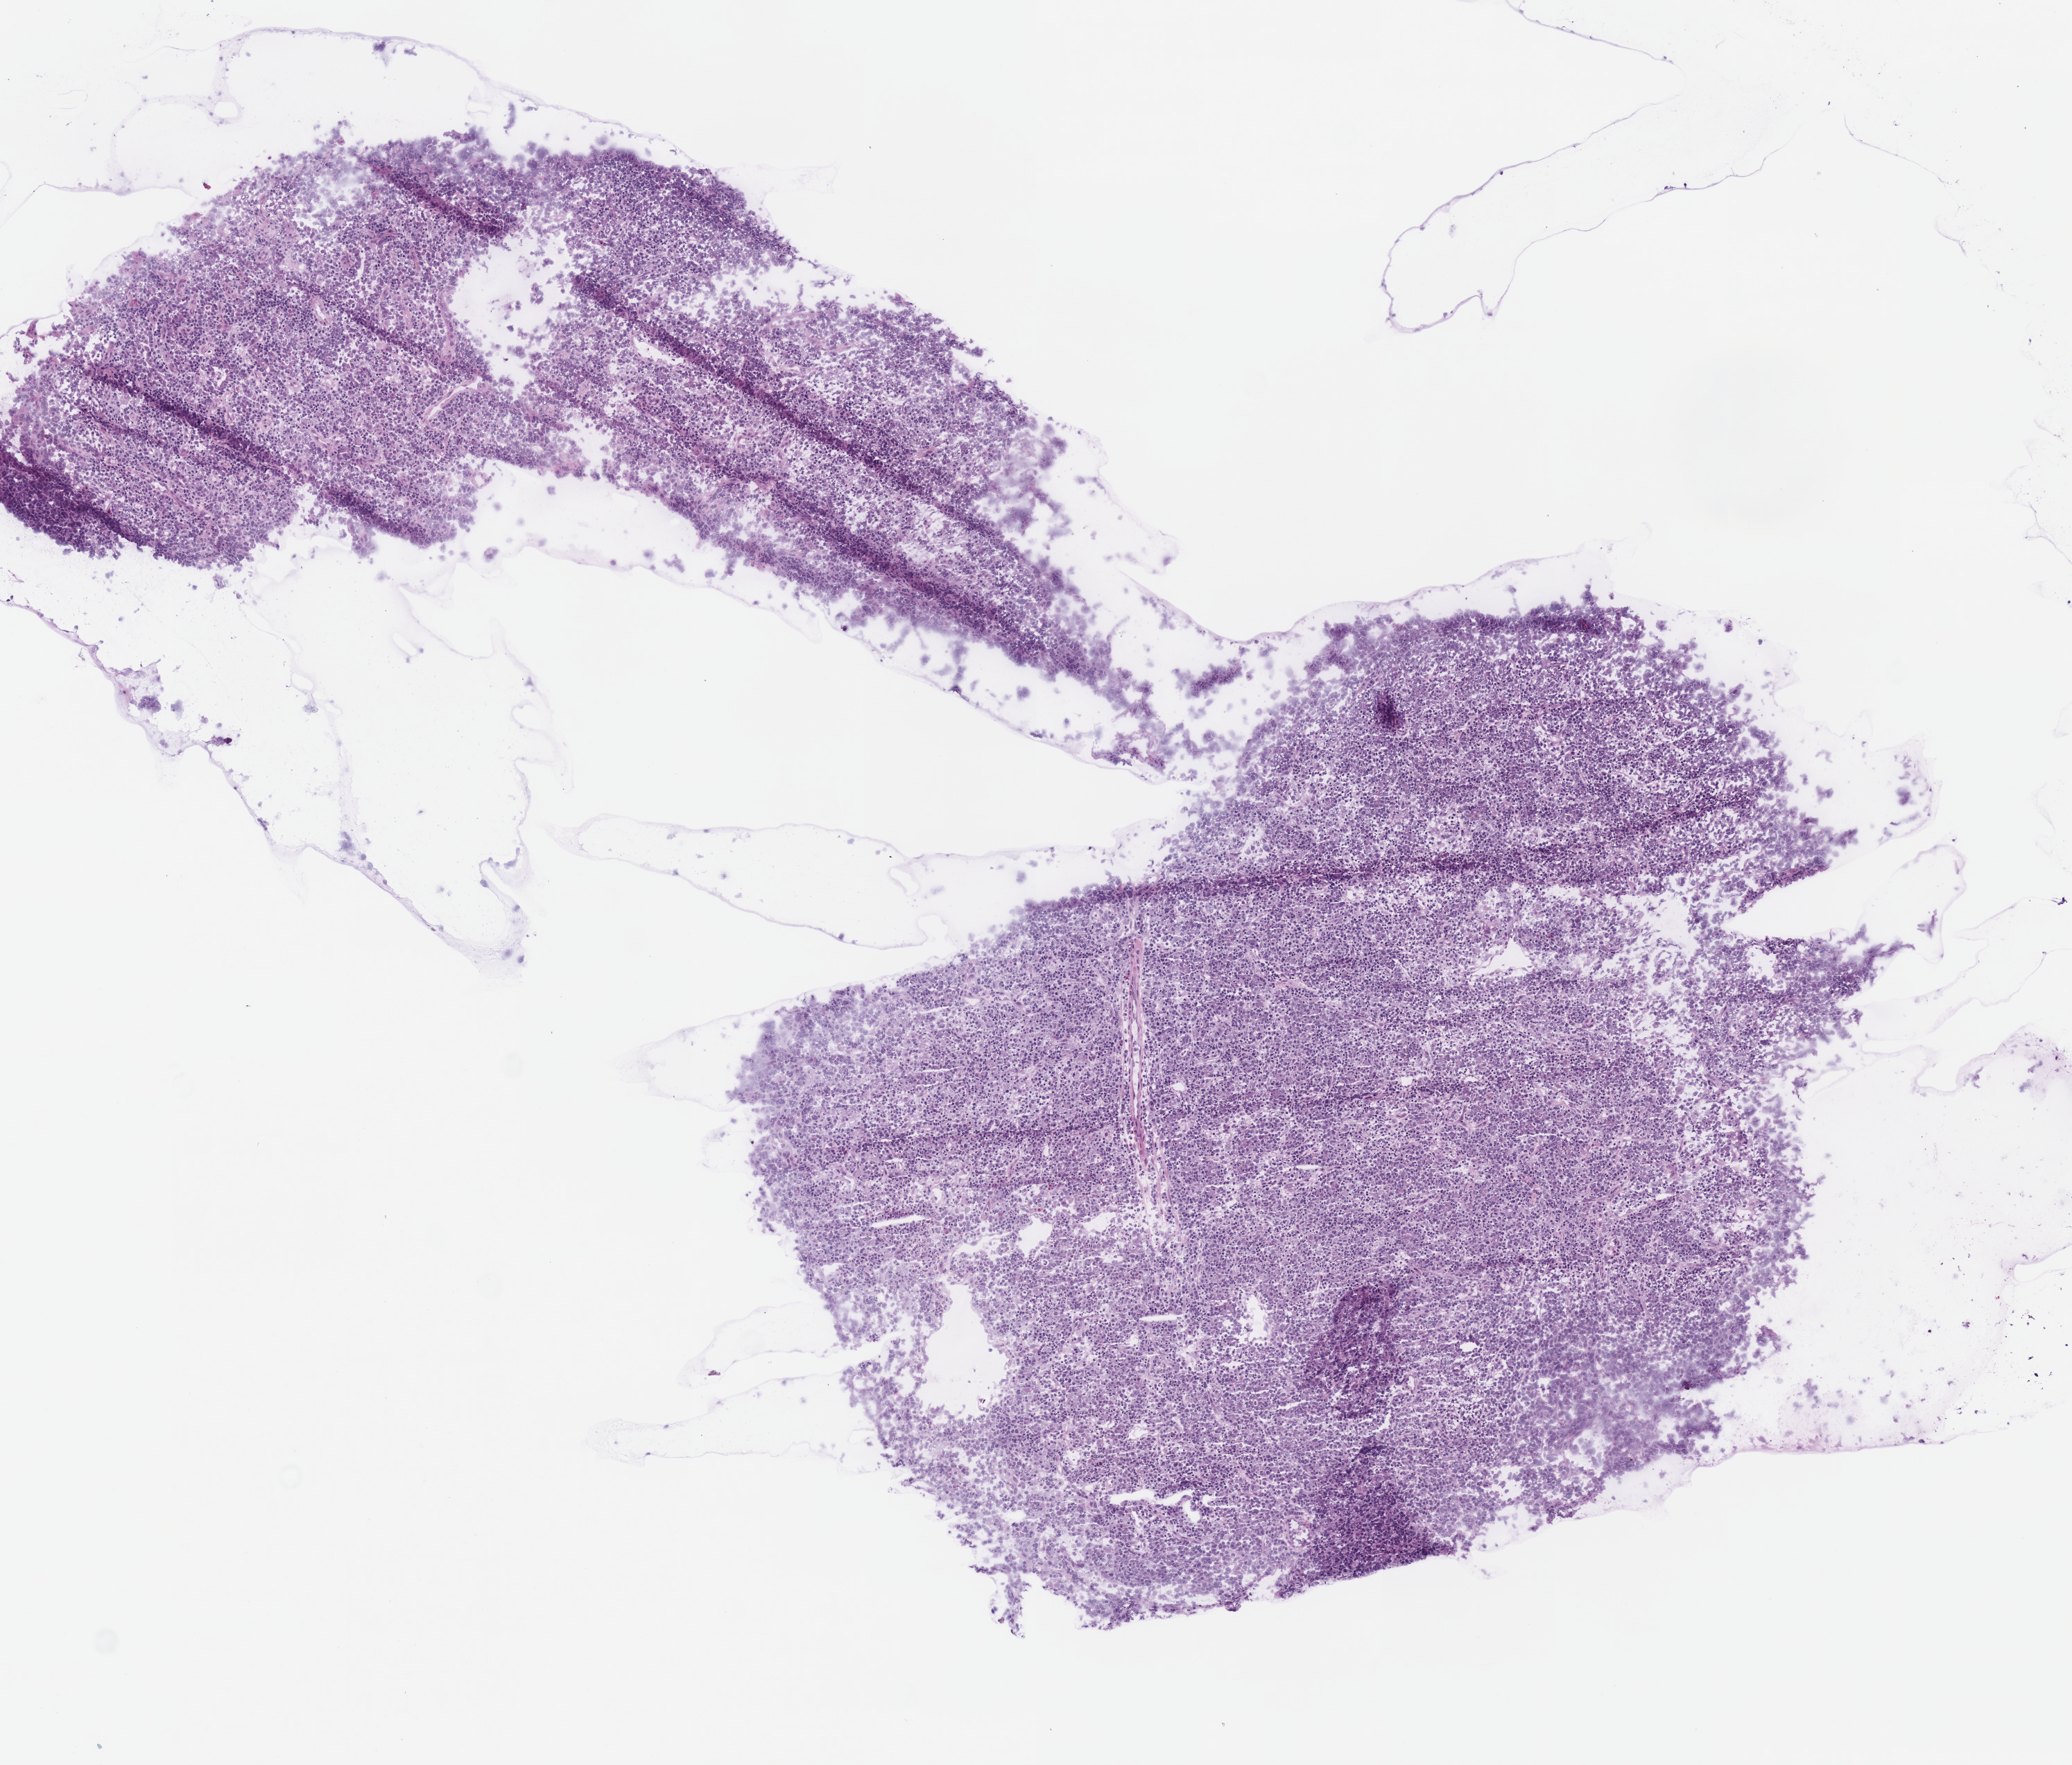
H&E-stained whole-slide image, a low-resolution overview of the entire scanned area, about 5.9 x 5.0 mm (slide scanned at 40x), frozen section from the top of the tissue portion, sample: primary tumour, stomach. Patient: male, age at initial diagnosis 70 years. Histologic grade: G3 (poorly differentiated). Slide review estimates, as recorded: tumour cells 95%, tumour nuclei 60%, normal cells 0%, stromal cells 5%, necrosis 0%.
- TNM: T4a N2 M0
- diagnosis: Carcinoma, diffuse type (body of stomach)
- AJCC pathologic stage: IIIB